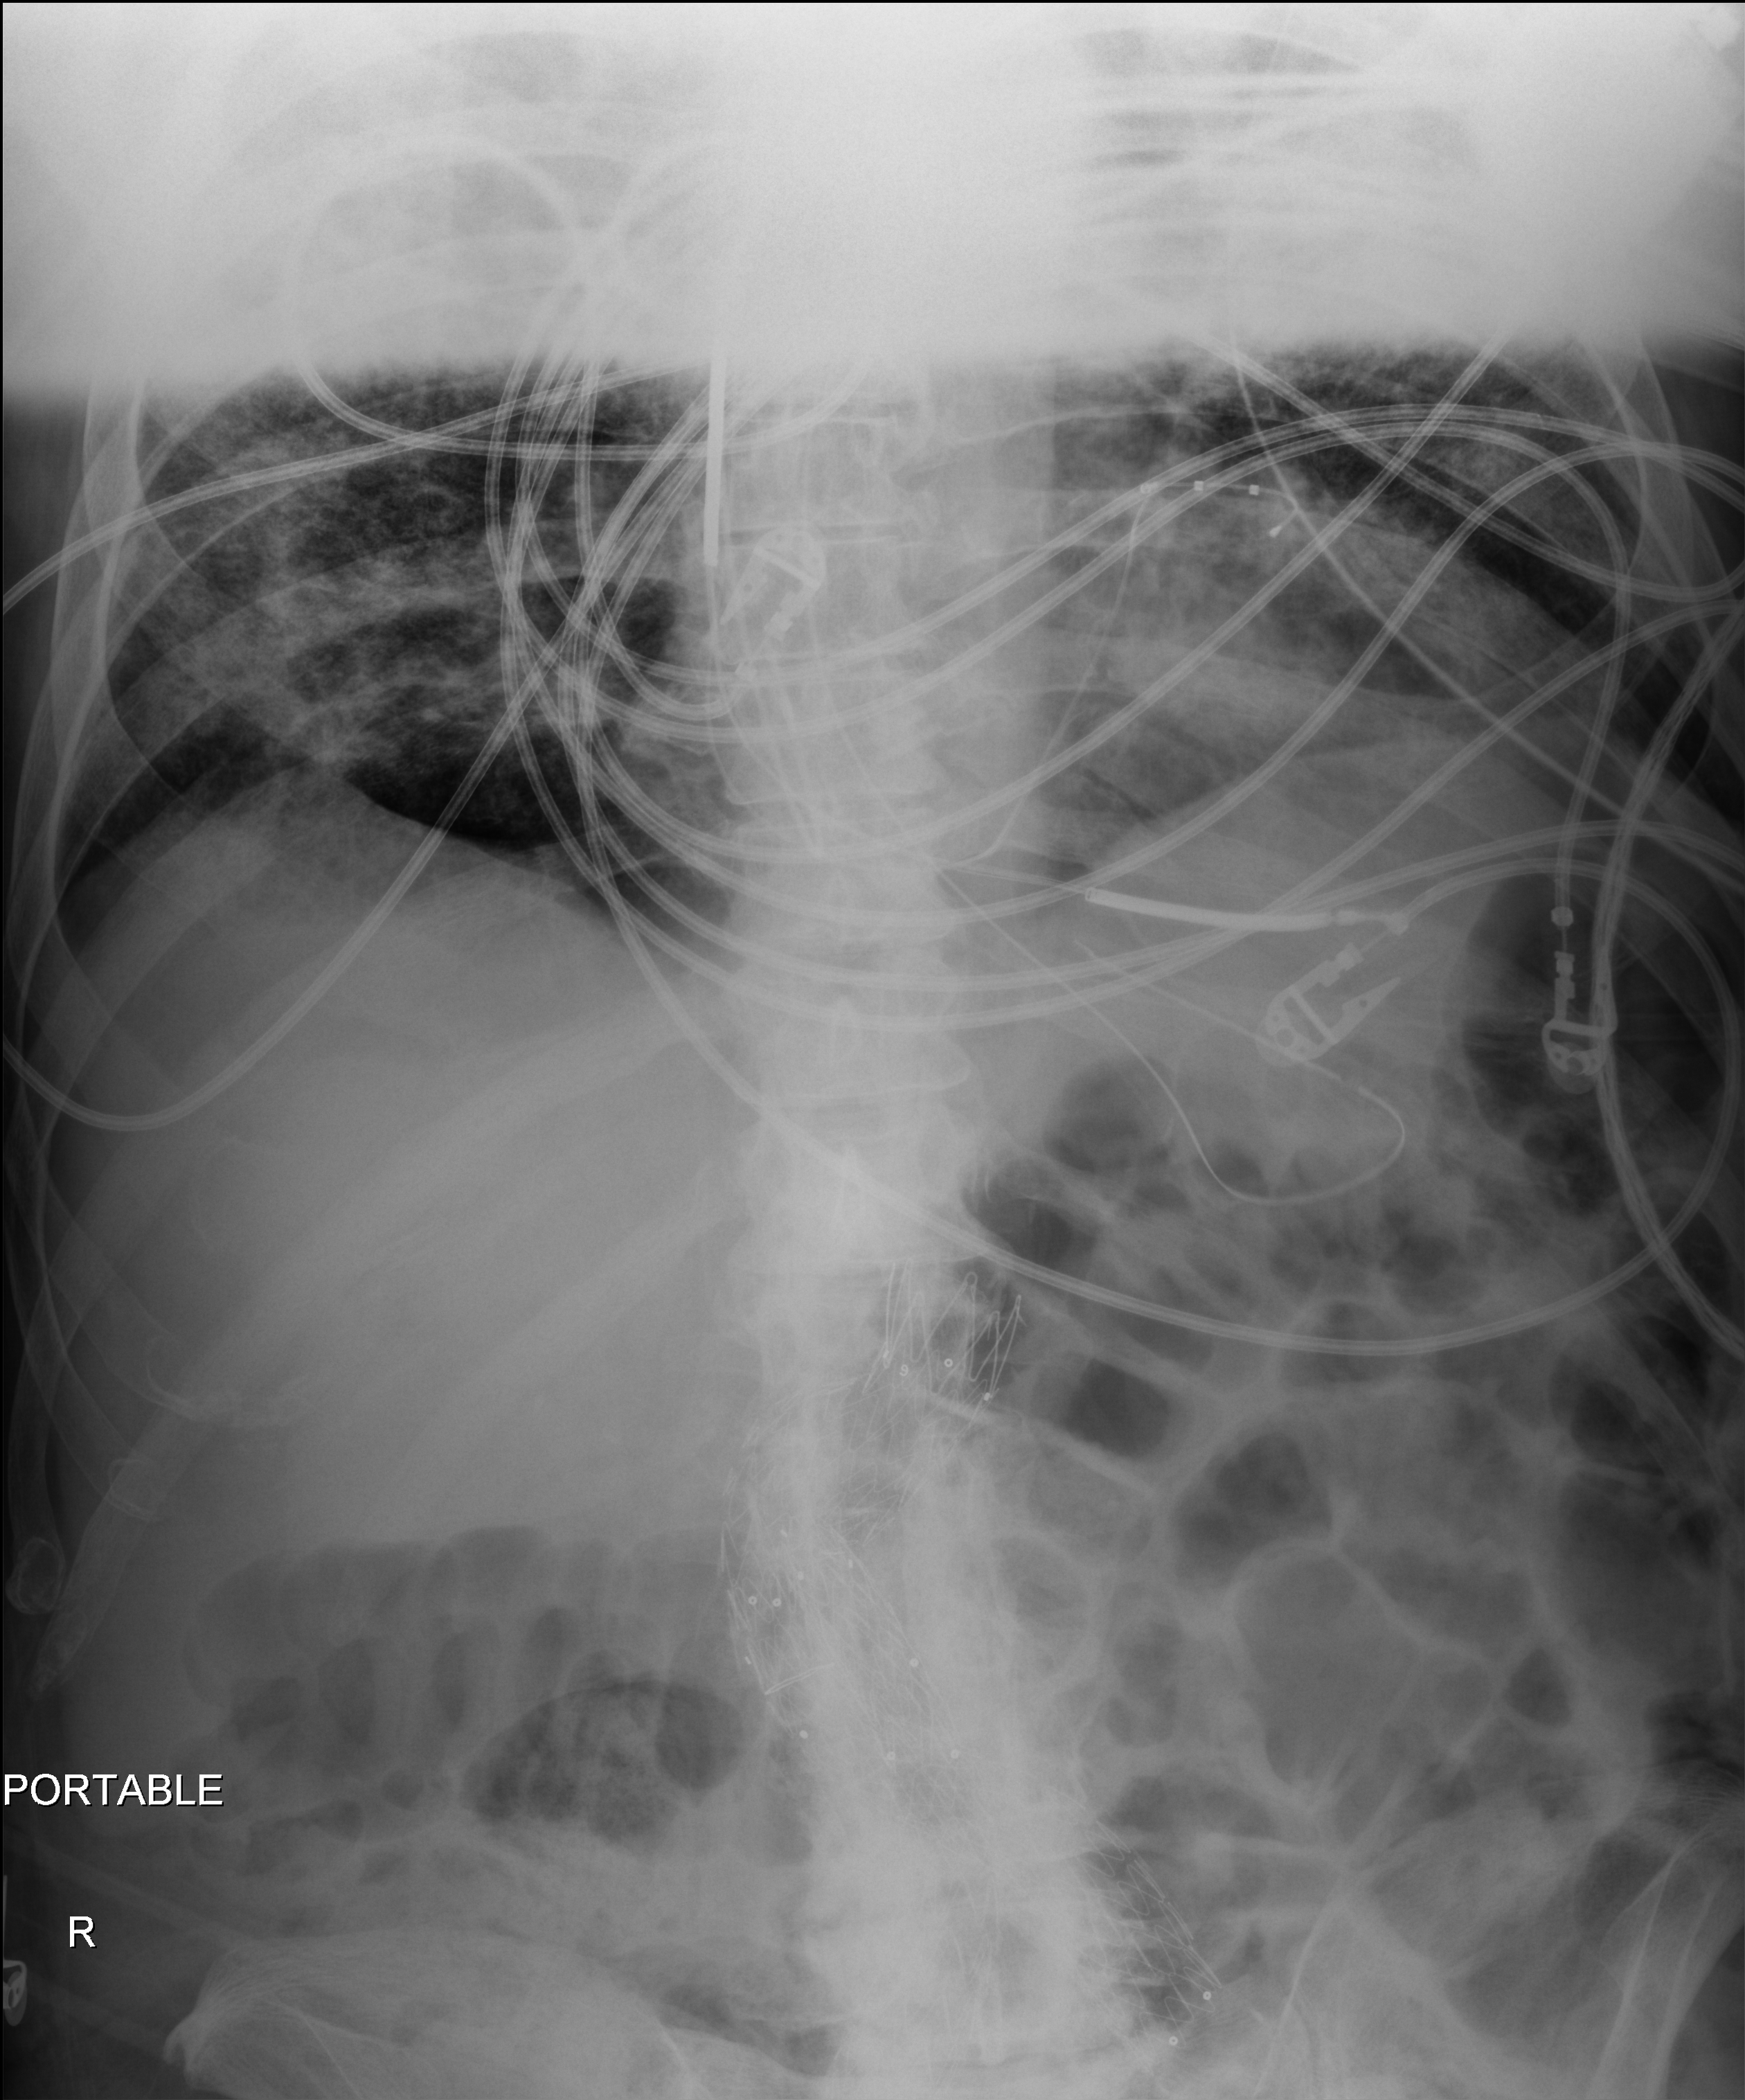
Abdomen X-ray (portable), anteroposterior (AP) projection. Patient hospitalised with COVID-19; male, aged 60–74 years.
Admission-level facts for this patient (not findings on this image; timing relative to this image not recorded):
- length of hospital stay: 36 days
- mechanically ventilated during this hospital stay: yes